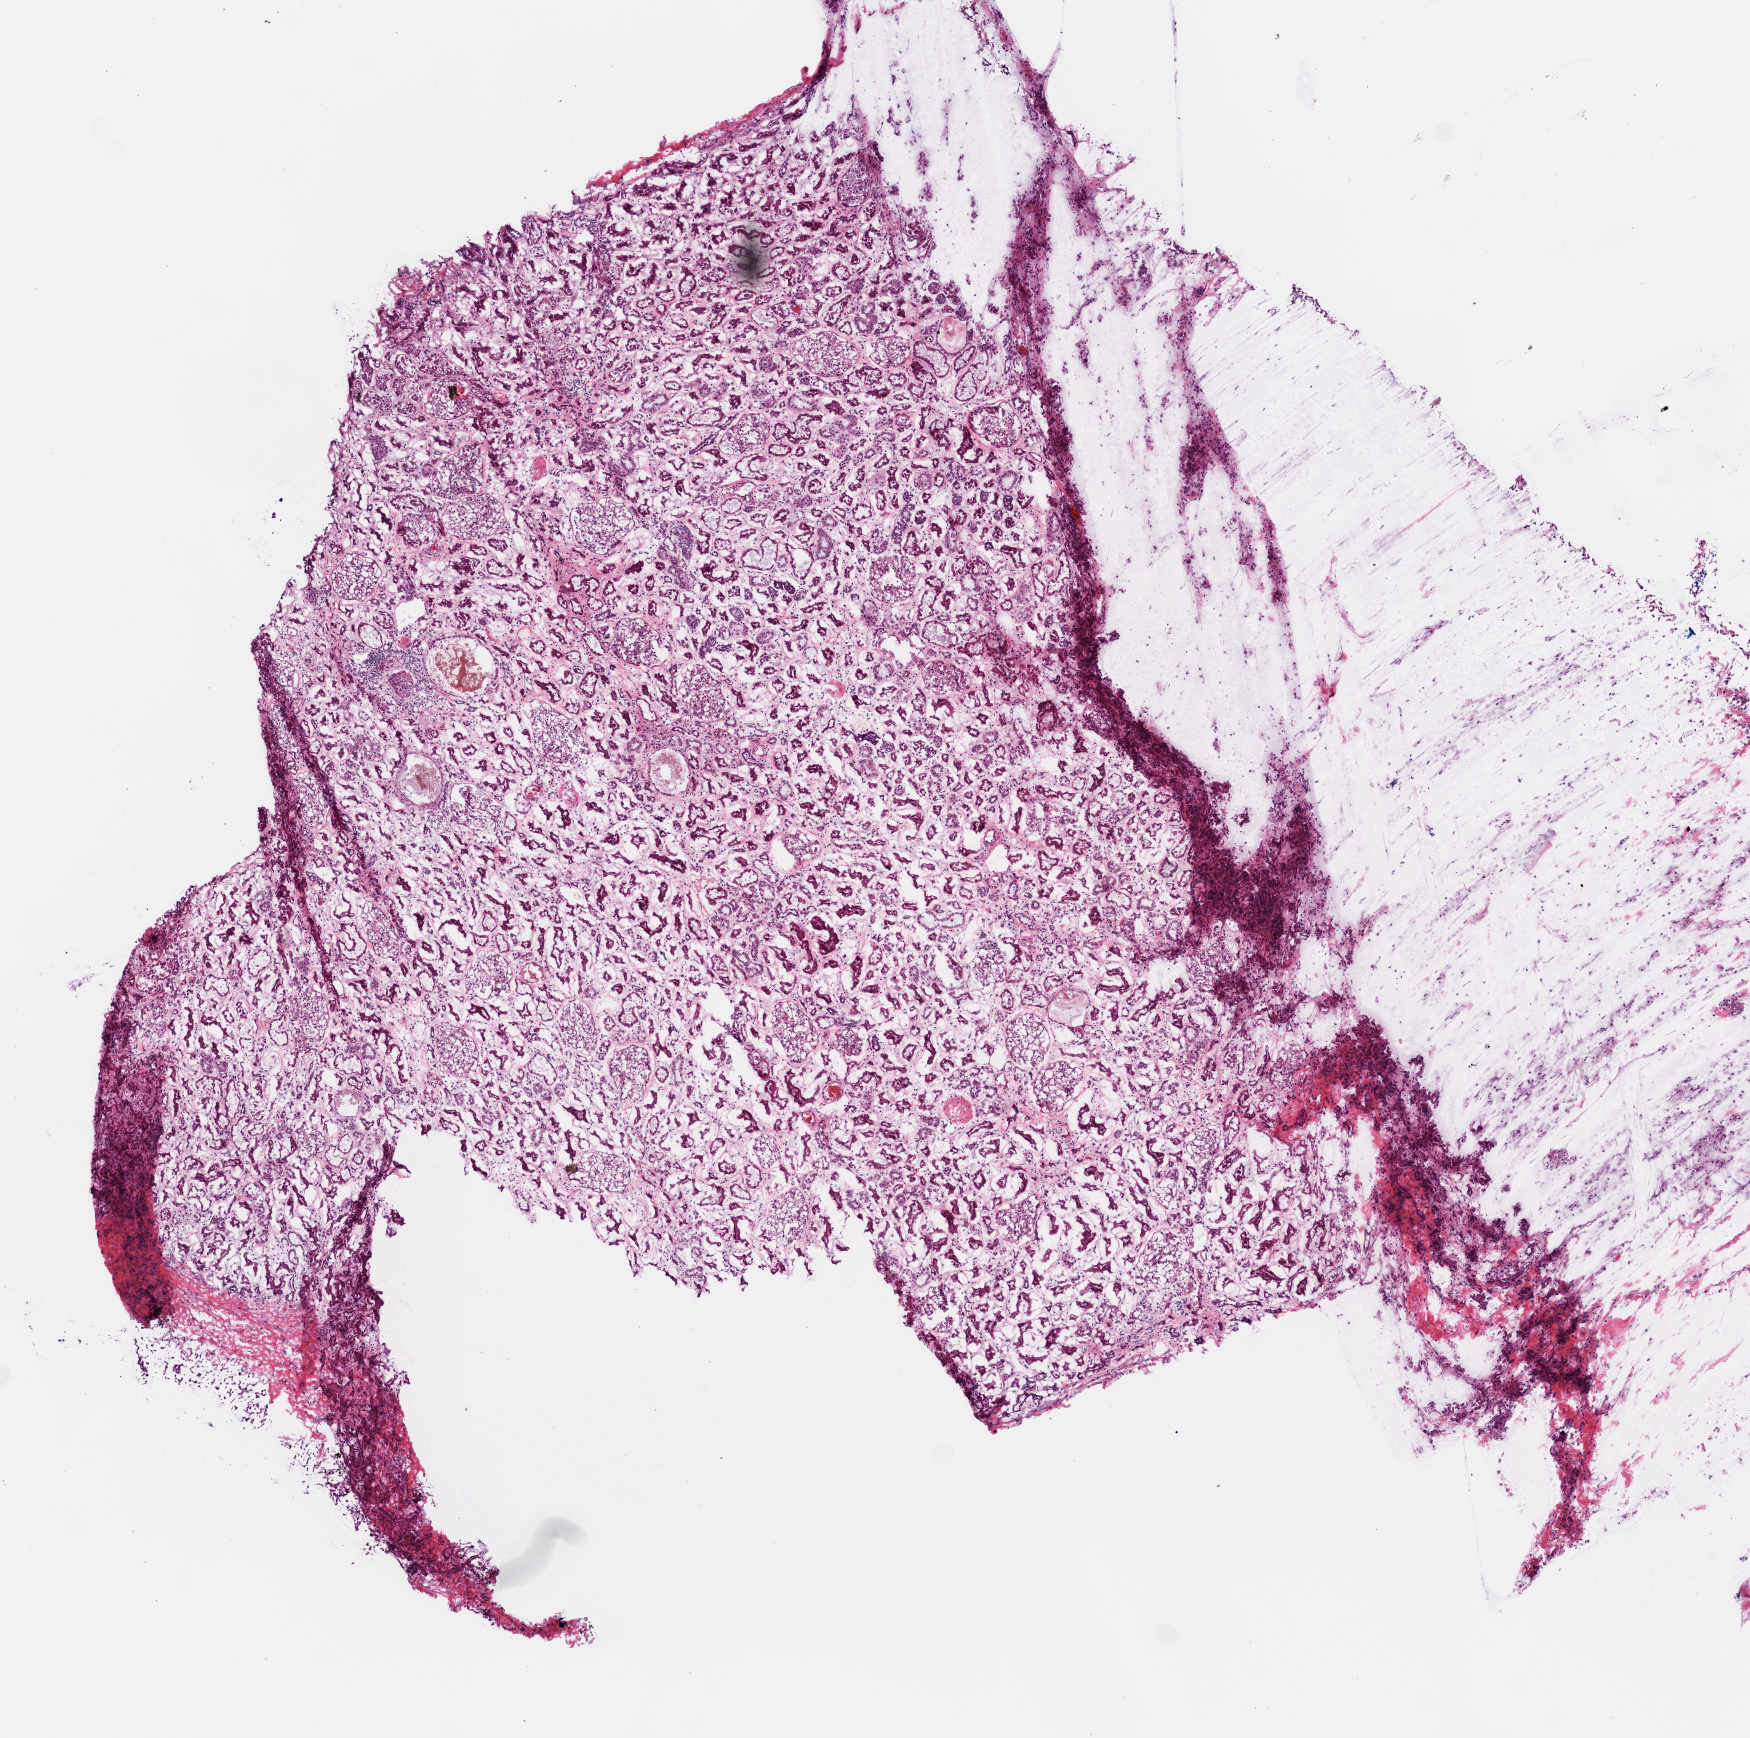
Digitized H&E-stained tissue section (whole slide) — a low-resolution overview of the entire scanned area, about 7.0 x 7.0 mm; frozen section from the top of the tissue portion; sample: solid tissue normal (non-tumour tissue), kidney. Male patient; age at initial diagnosis 41 years.
* this section: solid tissue normal (non-tumour) sample from the same patient
* patient diagnosis: Clear cell adenocarcinoma, NOS